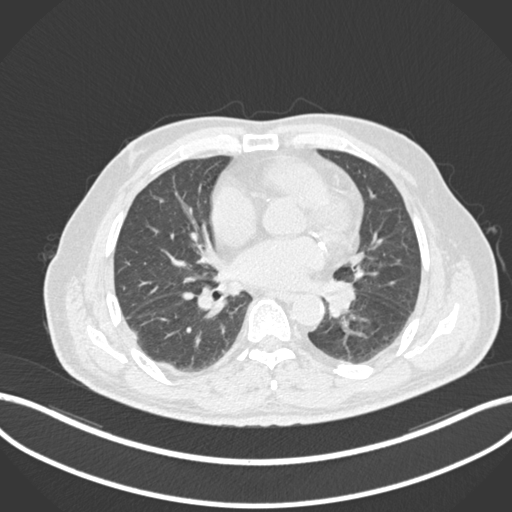
Chest CT, one axial slice; position 62 of 161 along the scan axis; lung window (W 1500 / L -600 HU); 512 × 512 image matrix, field of view 400 × 400 mm. Patient: male, 71 years. From the clinical record (not read from this slice): clinical TNM (as recorded): T1b N0 M0.
Structures marked on this image (bounding box drawn by a radiologist):
- lung tumour (recorded histology: squamous cell carcinoma): bounding box <325,280,360,323> (left, top, right, bottom; pixels)